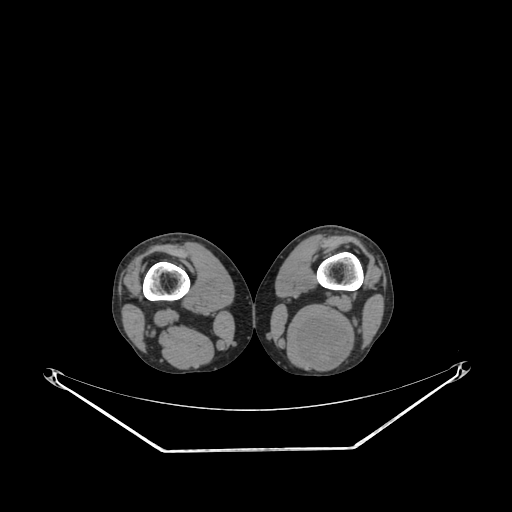
CT of an extremity soft-tissue mass (from a PET/CT study), one axial slice; slice 195 of 267 in the series (ordered by position); 140 kVp; soft-tissue window (W 400 / L 40 HU); 3.75 mm slice thickness; 512 × 512 image matrix, field of view 500 × 500 mm. Male patient. From the clinical record (not read from this slice): histological type: synovial sarcoma; site of the primary tumour: left poplietal fossa.
Structures marked on this image (expert contour drawn on MRI and transferred to this co-registered scan by the dataset authors):
- gross tumour volume (mass): box from (x=292, y=317) to (x=350, y=369) px